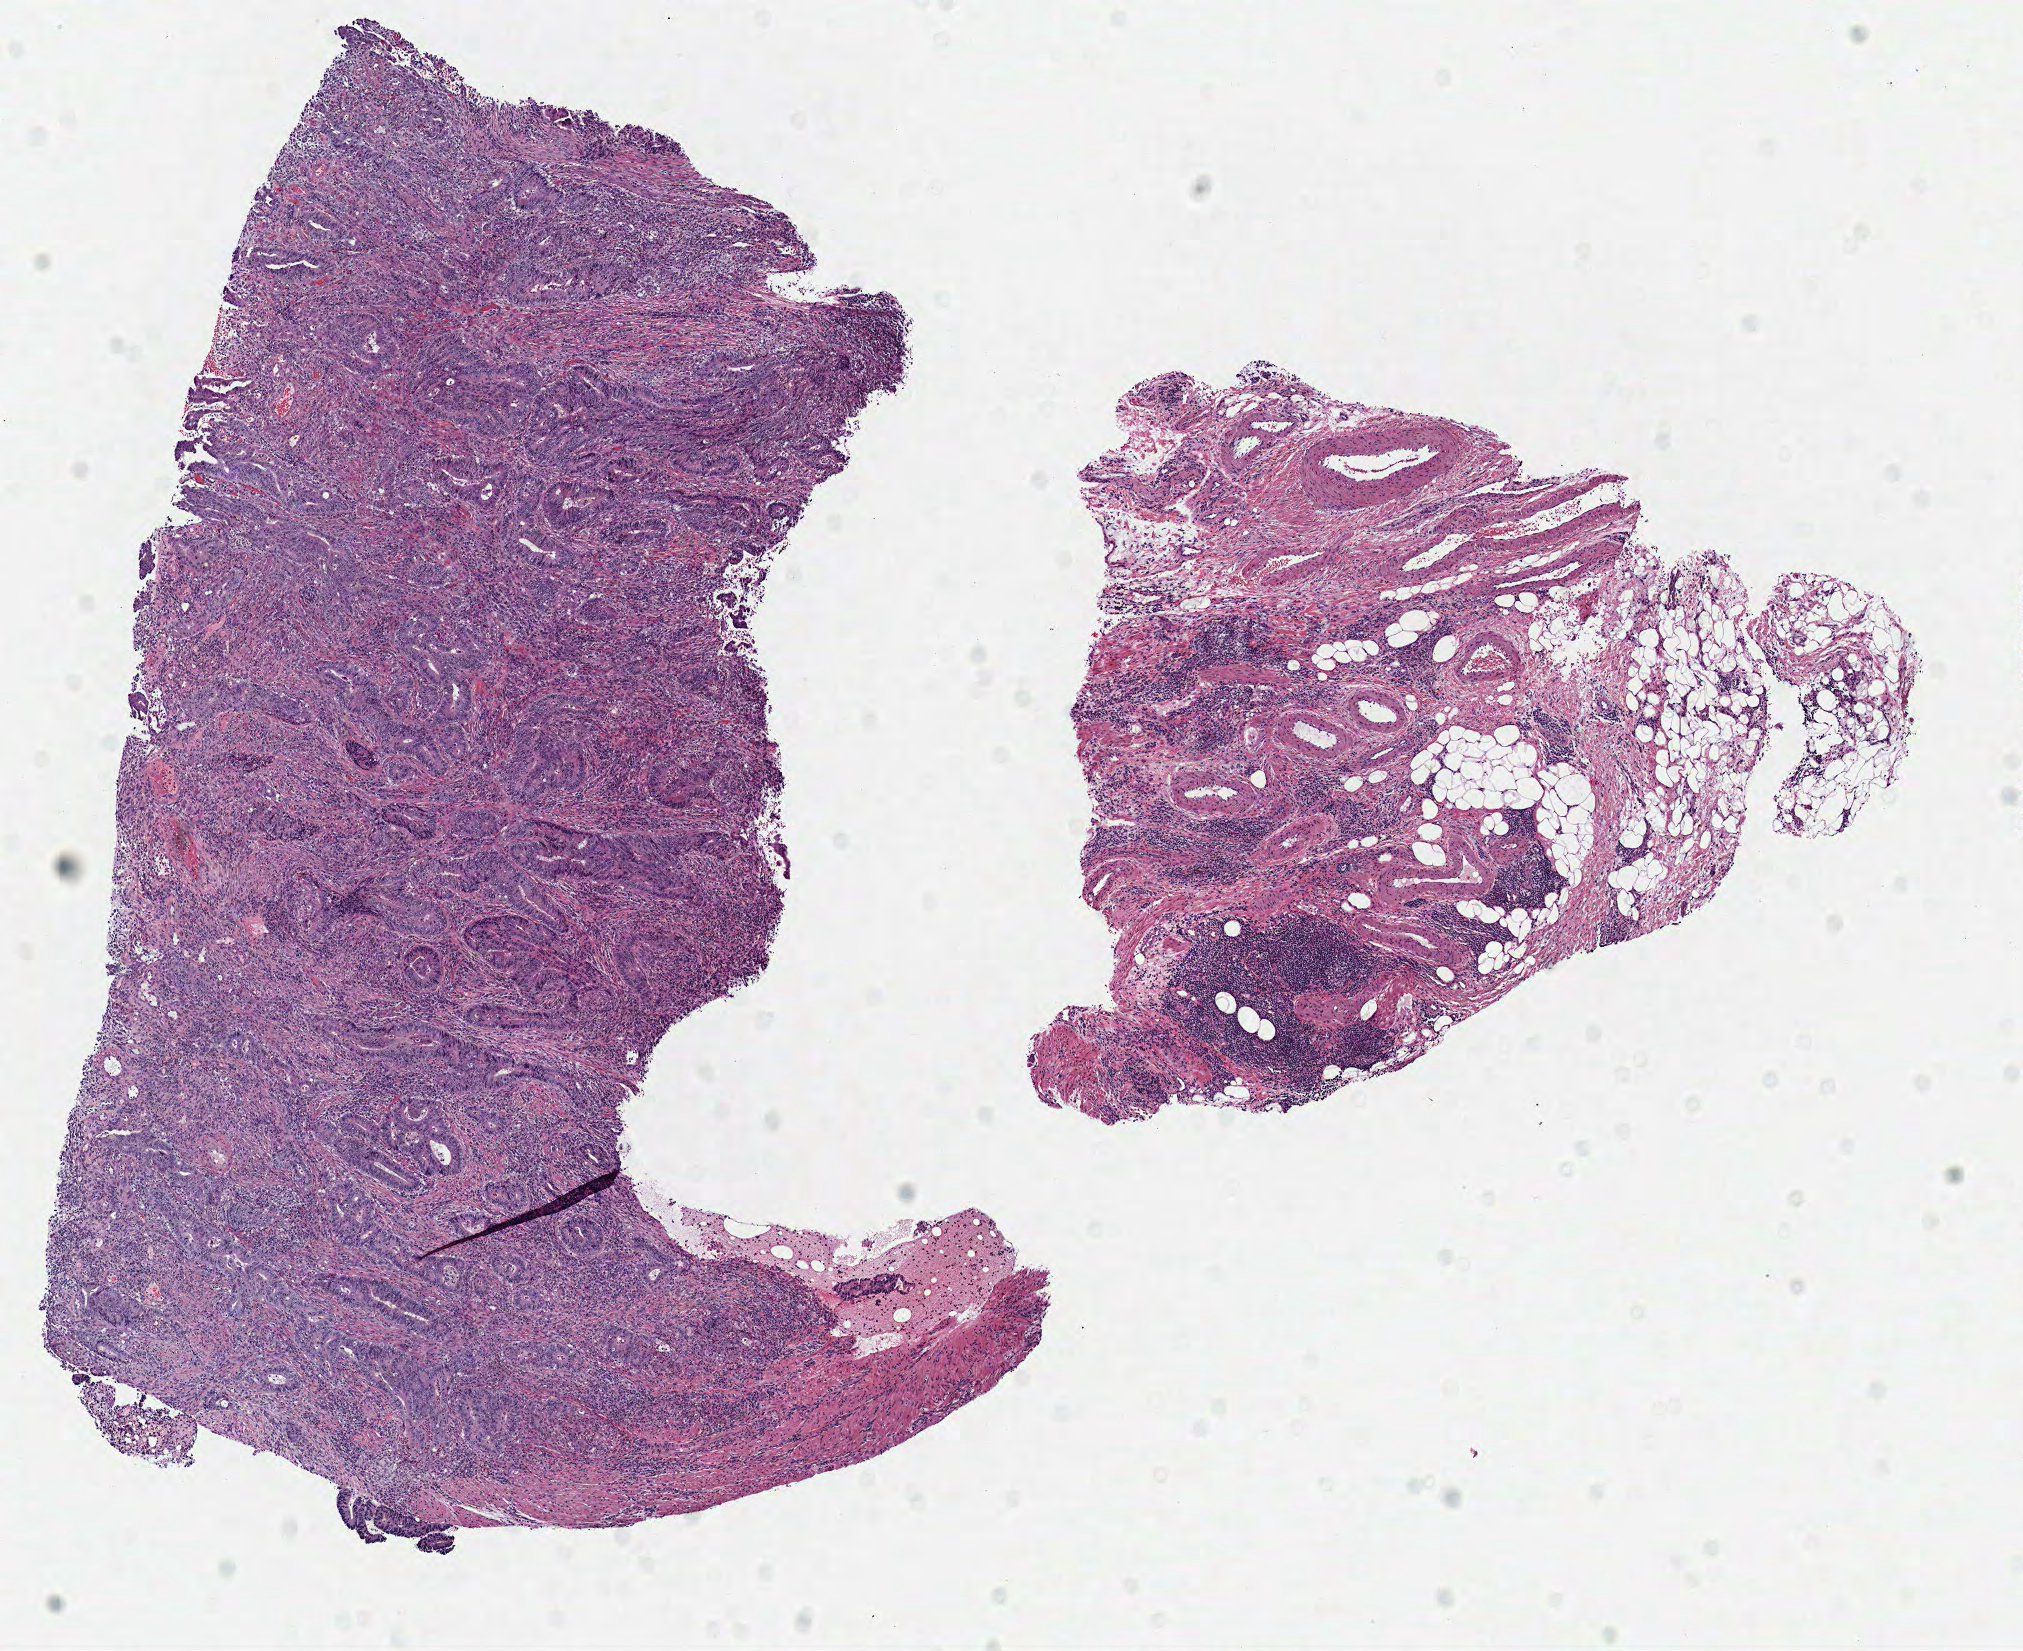
H&E-stained whole-slide image — whole scanned area (about 8.0 x 6.5 mm) shown as a low-resolution overview, frozen section from the top of the tissue portion, primary tumour sample from the colon. Male patient; age at initial diagnosis 61 years. Slide review estimates, as recorded: tumour cells 65%, tumour nuclei 70%, normal cells 0%, stromal cells 35%, necrosis 0%. Infiltration values recorded for this section: lymphocyte infiltration 10%, monocyte infiltration 0%, neutrophil infiltration 7%.
Lymph nodes positive (case pathology): 0 of 24 examined. Diagnosis: Adenocarcinoma, NOS (cecum). AJCC pathologic stage: I.